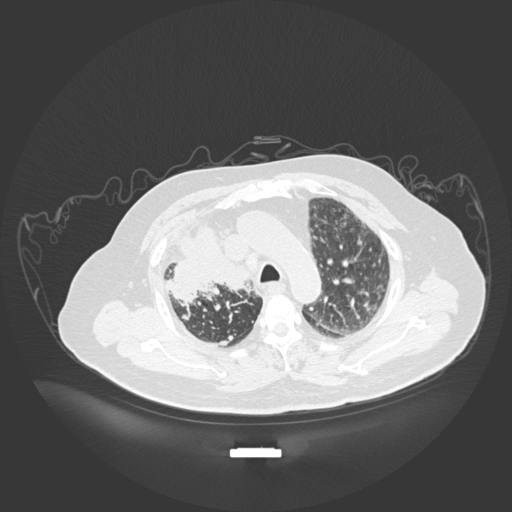
Chest CT, one axial slice; 120 kVp; lung window (W 1500 / L -600 HU); 512 × 512 image matrix, field of view 500 × 500 mm. Patient: male, 69 years. From the clinical record (not read from this slice): clinical TNM (as recorded): T4 N3 M1.
Outlined on this slice (bounding box drawn by a radiologist):
- lung tumour (recorded histology: adenocarcinoma): box from (x=168, y=221) to (x=251, y=307) px